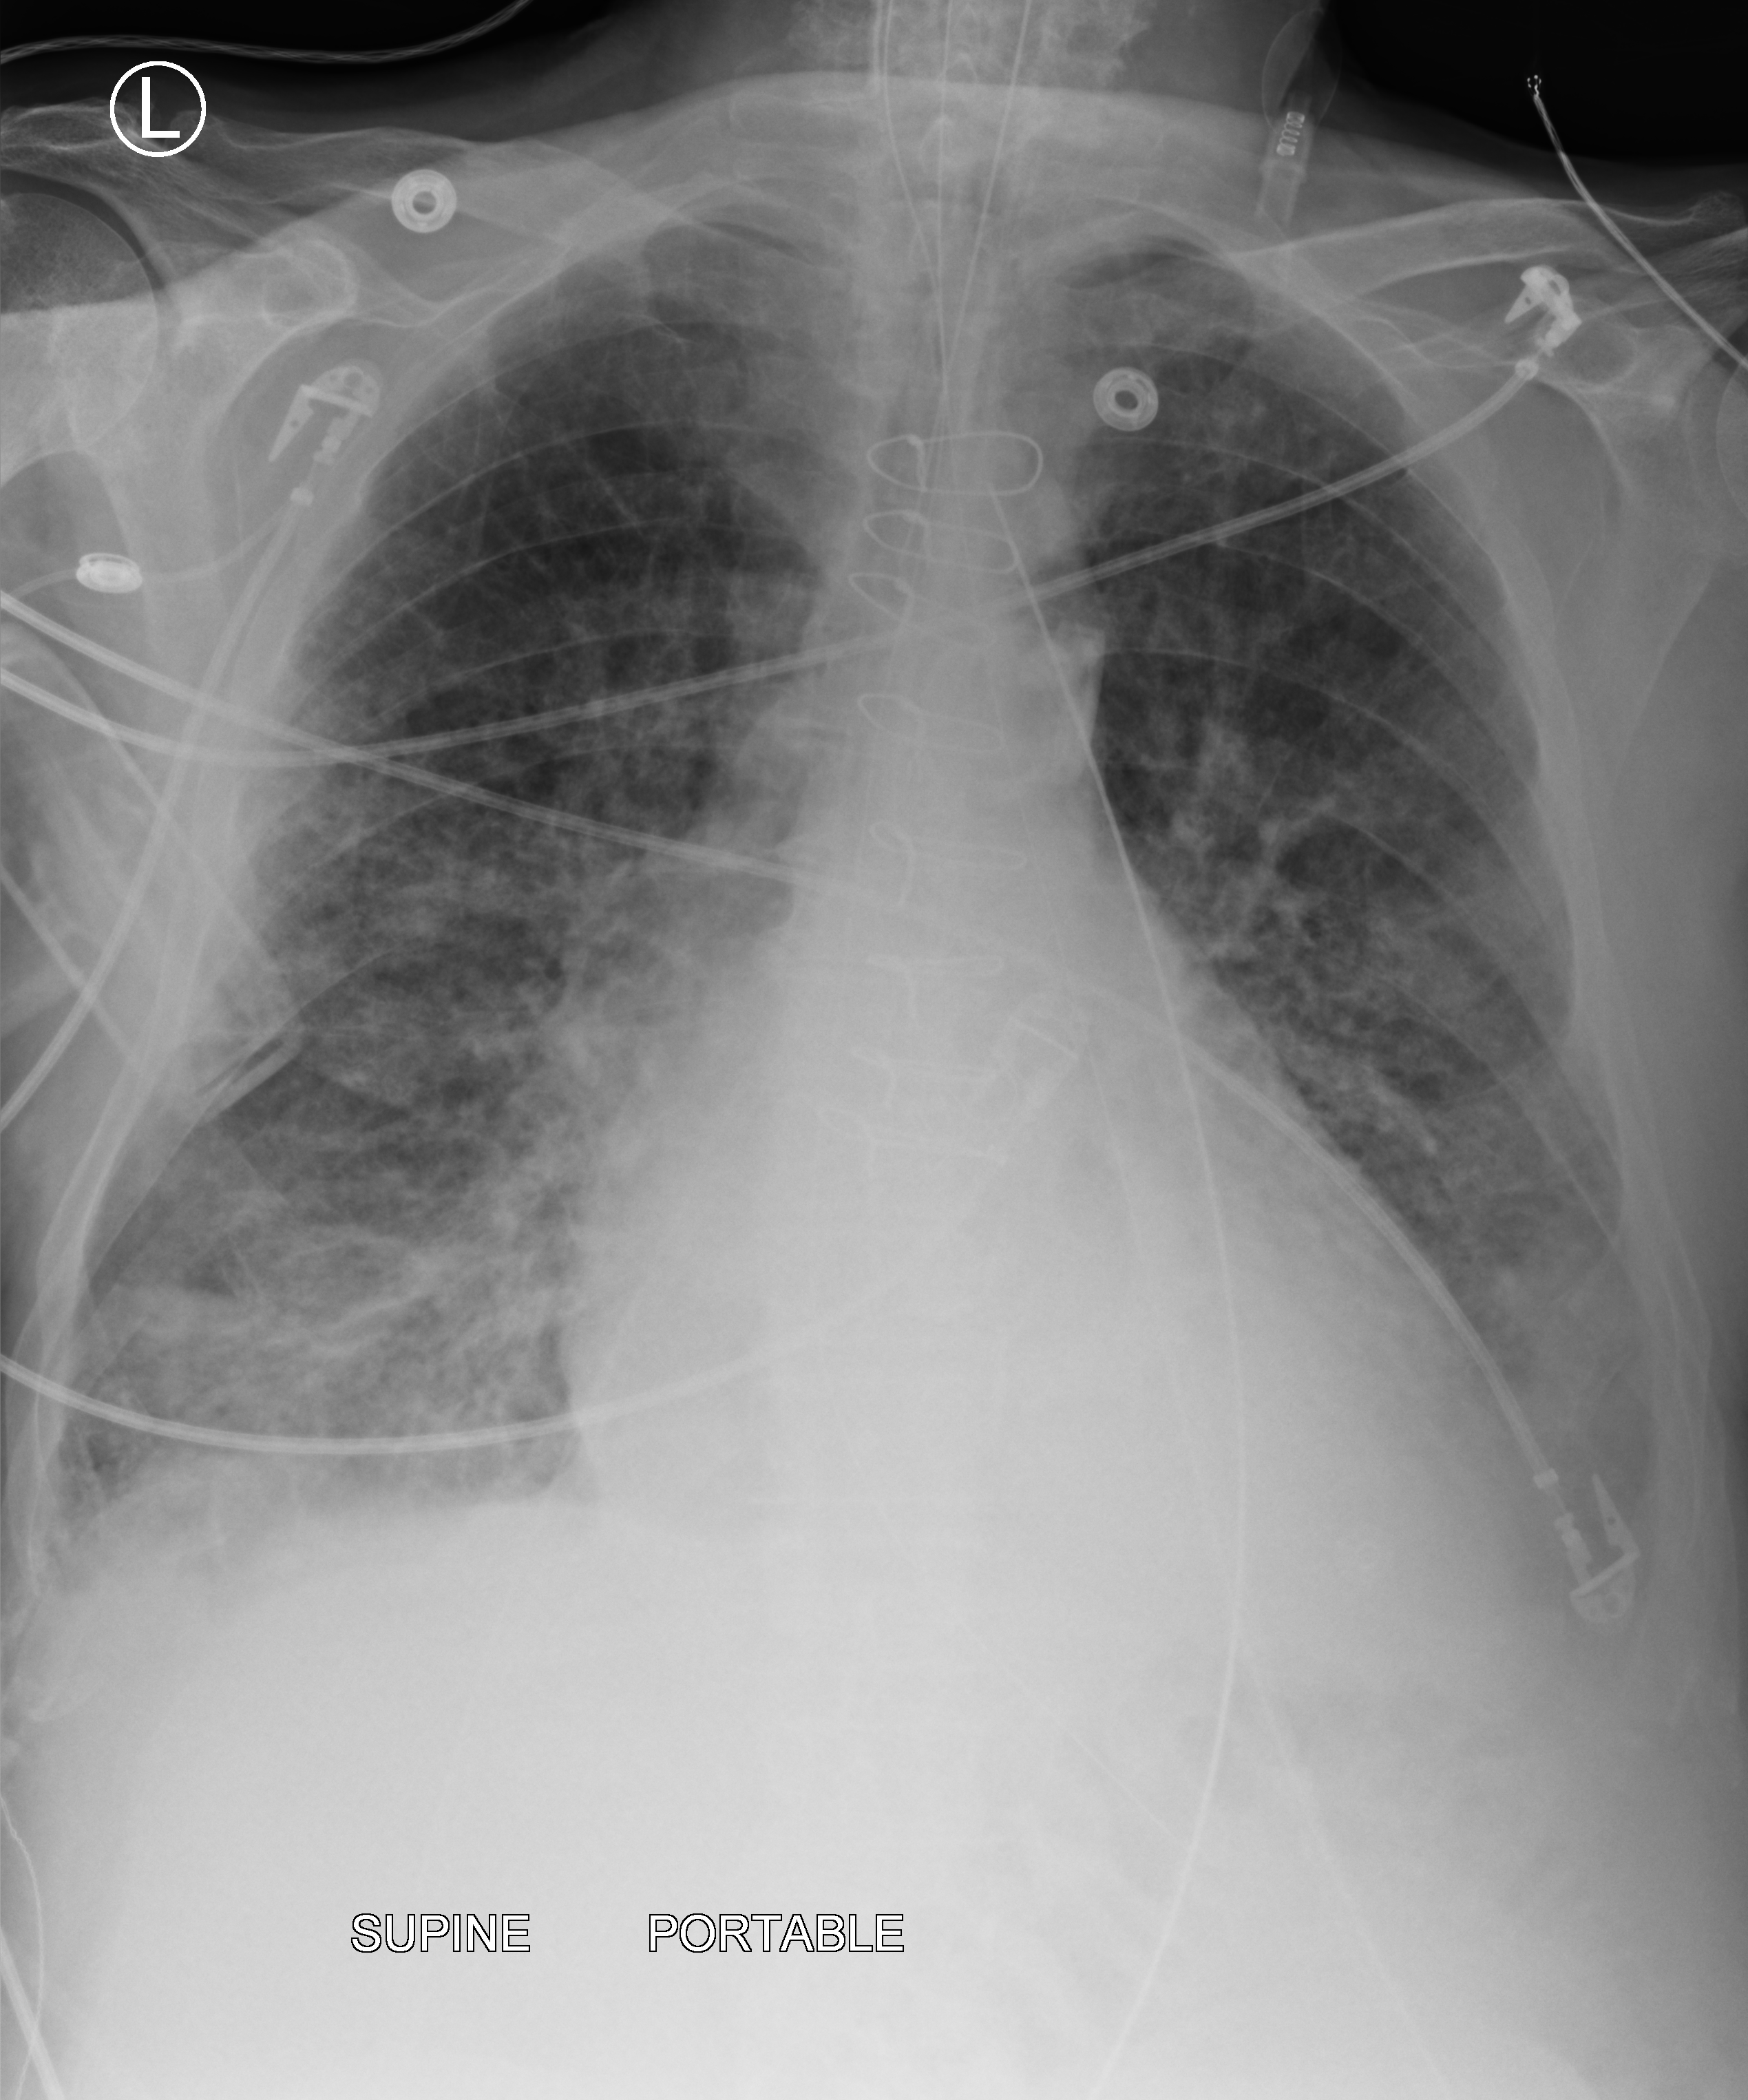
Chest X-ray (portable); anteroposterior (AP) projection. Patient hospitalised with COVID-19; male, aged 75–90 years.
From the hospital-stay record, not from the radiograph (when in the stay this image was taken is not recorded):
- mechanically ventilated during this hospital stay: yes